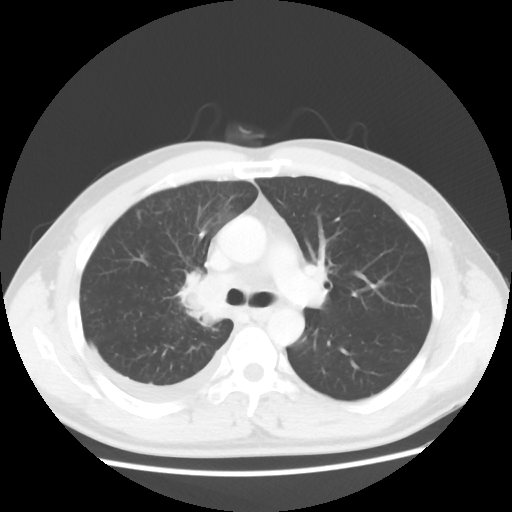
Chest CT, one axial slice; slice 35 of 56 in the series (ordered by position); 120 kVp; lung window (W 1500 / L -600 HU); 5 mm slice thickness; 512 × 512 image matrix, field of view 360 × 360 mm. Patient: male, 46 years. Case-level facts recorded for this patient, not image findings: clinical TNM (as recorded): T2 N3 M1.
Annotated regions visible in this slice (bounding box drawn by a radiologist):
- lung tumour (recorded histology: adenocarcinoma): bounding box <189,274,238,321> (left, top, right, bottom; pixels)